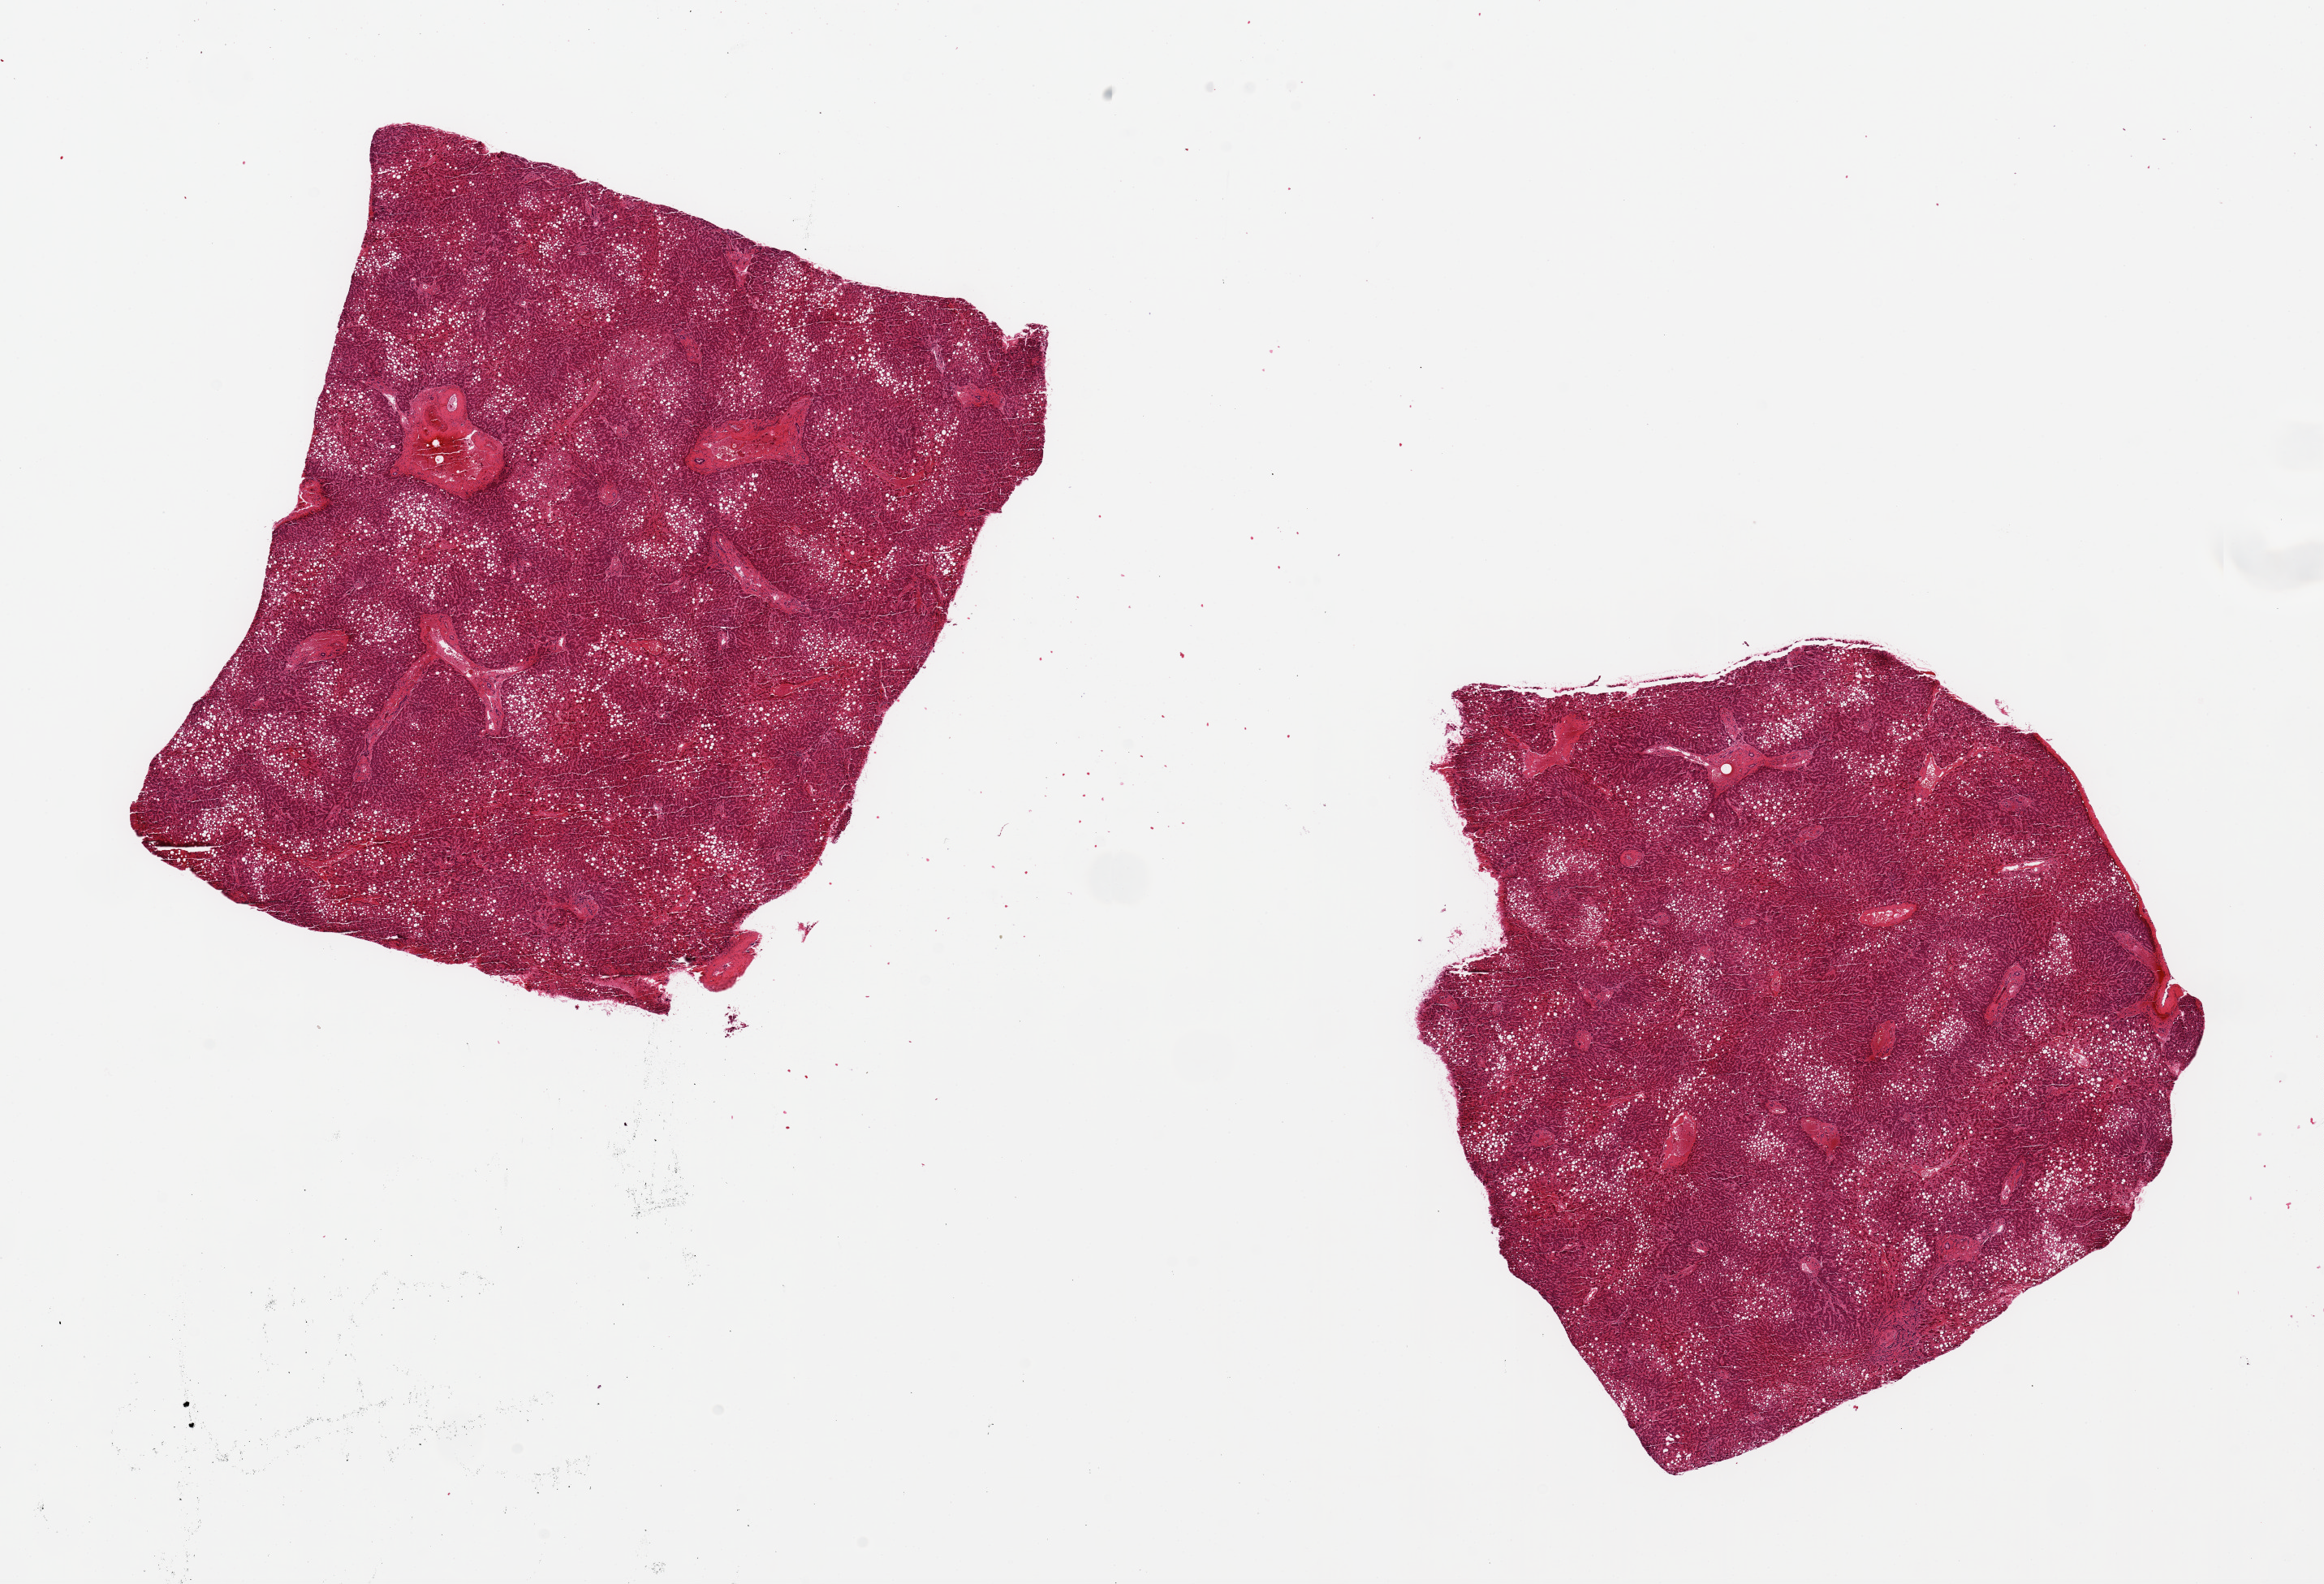
Haematoxylin and eosin whole-slide image — a low-resolution overview of the entire scanned area, about 22.6 x 15.4 mm. PAXgene-fixed, paraffin-embedded tissue. Target tissue: liver. Donor tissue sample.
Pathologist's review note for this sample: 2 pieces, 8x7 & 8x7mm; 30% macrovesicular steatosis. Moderate congestion.